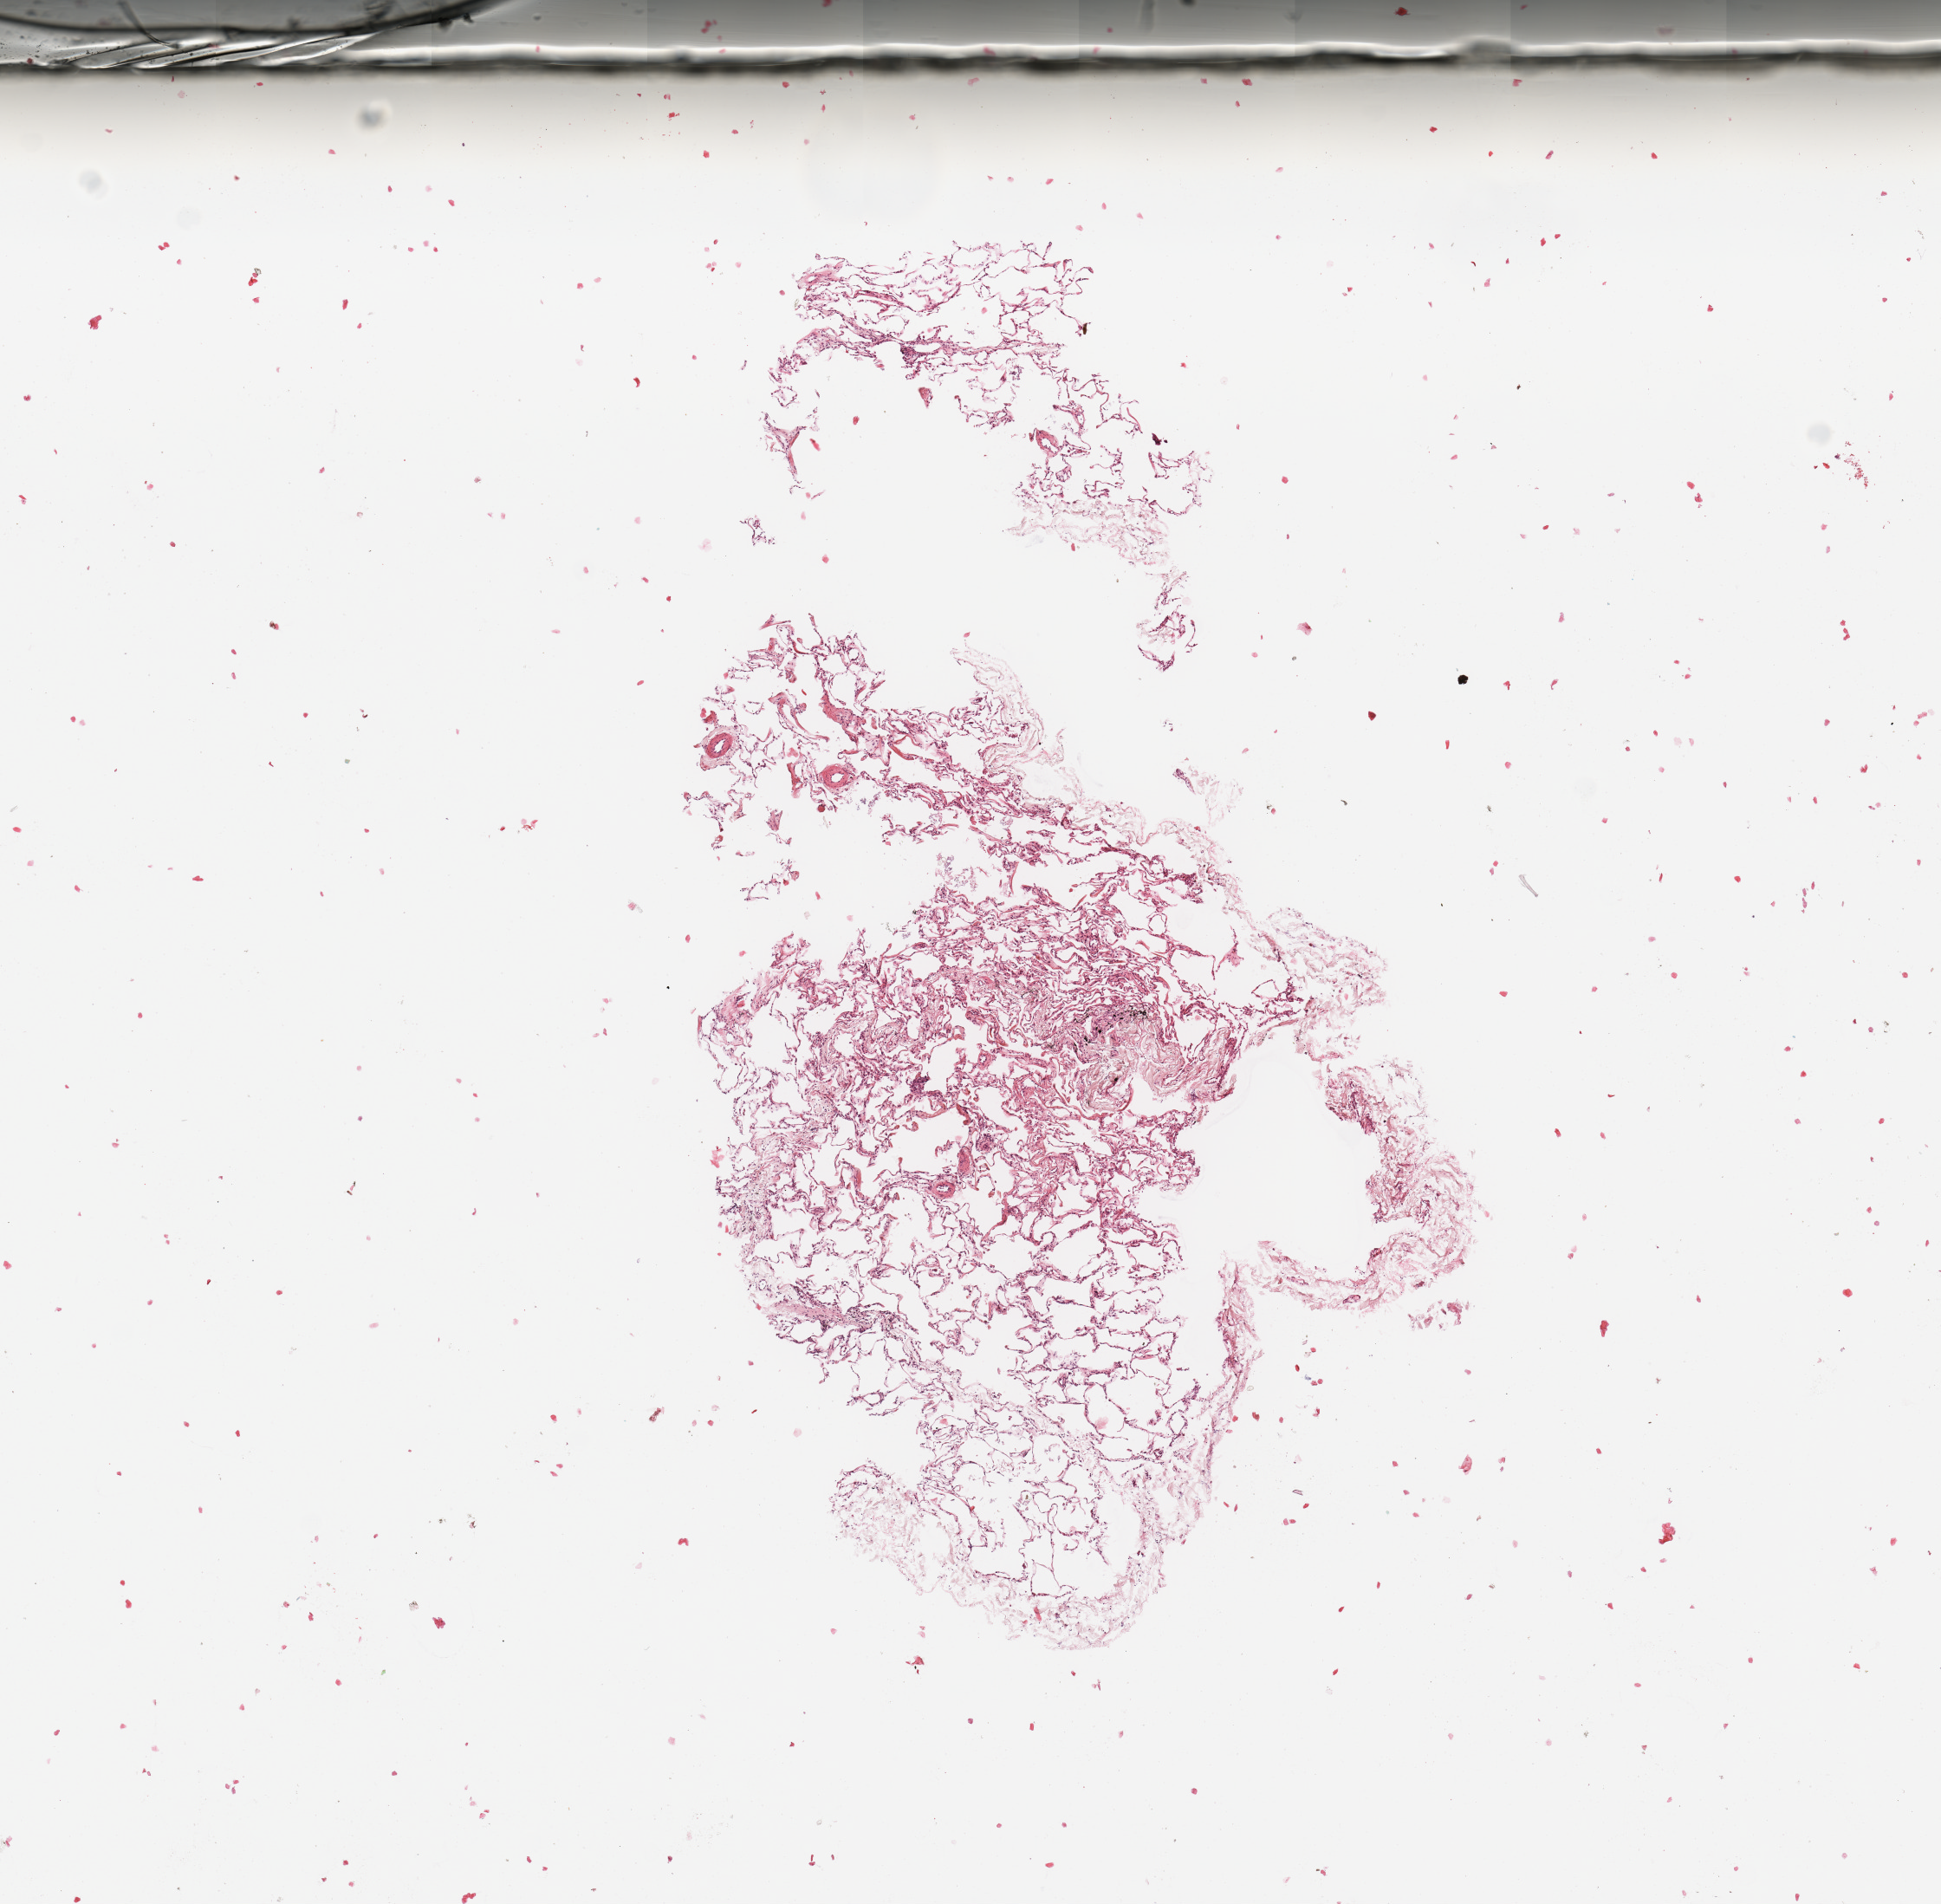
Whole-slide histology image, Hematoxylin and eosin (H&E) stained, low-resolution overview of the scanned area, about 8.9 x 8.7 mm (acquisition: 20x scan), normal (non-tumour) tissue sample, sampled site: lung. Male, 69 y/o.
This section: normal (non-tumour) tissue from the same patient. Patient diagnosis: Adenocarcinoma, NOS.